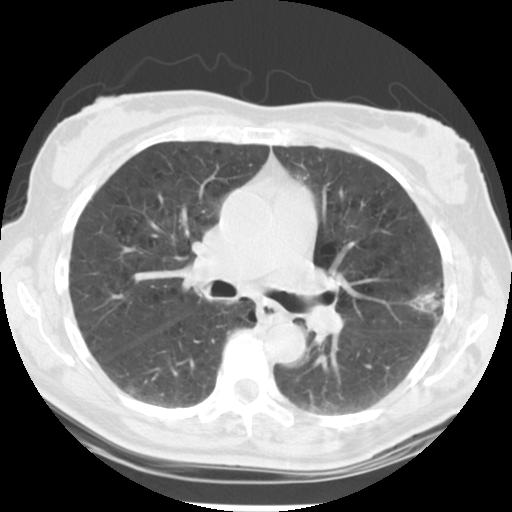
Chest CT (low-dose screening protocol), one axial image. Second screening round (one year after baseline). Lung window (W 1500 / L -600 HU). Standard (soft-tissue) reconstruction kernel (STANDARD). 120 kVp. Female participant, aged 61 years at enrolment. Current smoker at enrolment.
- Lesion marked by an expert reader, bounding box <404,276,464,337> (left, top, right, bottom; pixels).
- Screening reader's record for this exam (one nodule recorded; not confirmed to be the boxed lesion): non-calcified nodule or mass ≥4 mm, left upper lobe, 15 × 15 mm, poorly defined margins, mixed attenuation, pre-existing on the prior screen: no.
- Official screen result: positive, other.
- Lung cancer was diagnosed 152 days after this screen: bronchiolo-alveolar adenocarcinoma, NOS, left upper lobe, well differentiated (G1), stage IA (AJCC 6th edition), 11 mm at pathology.